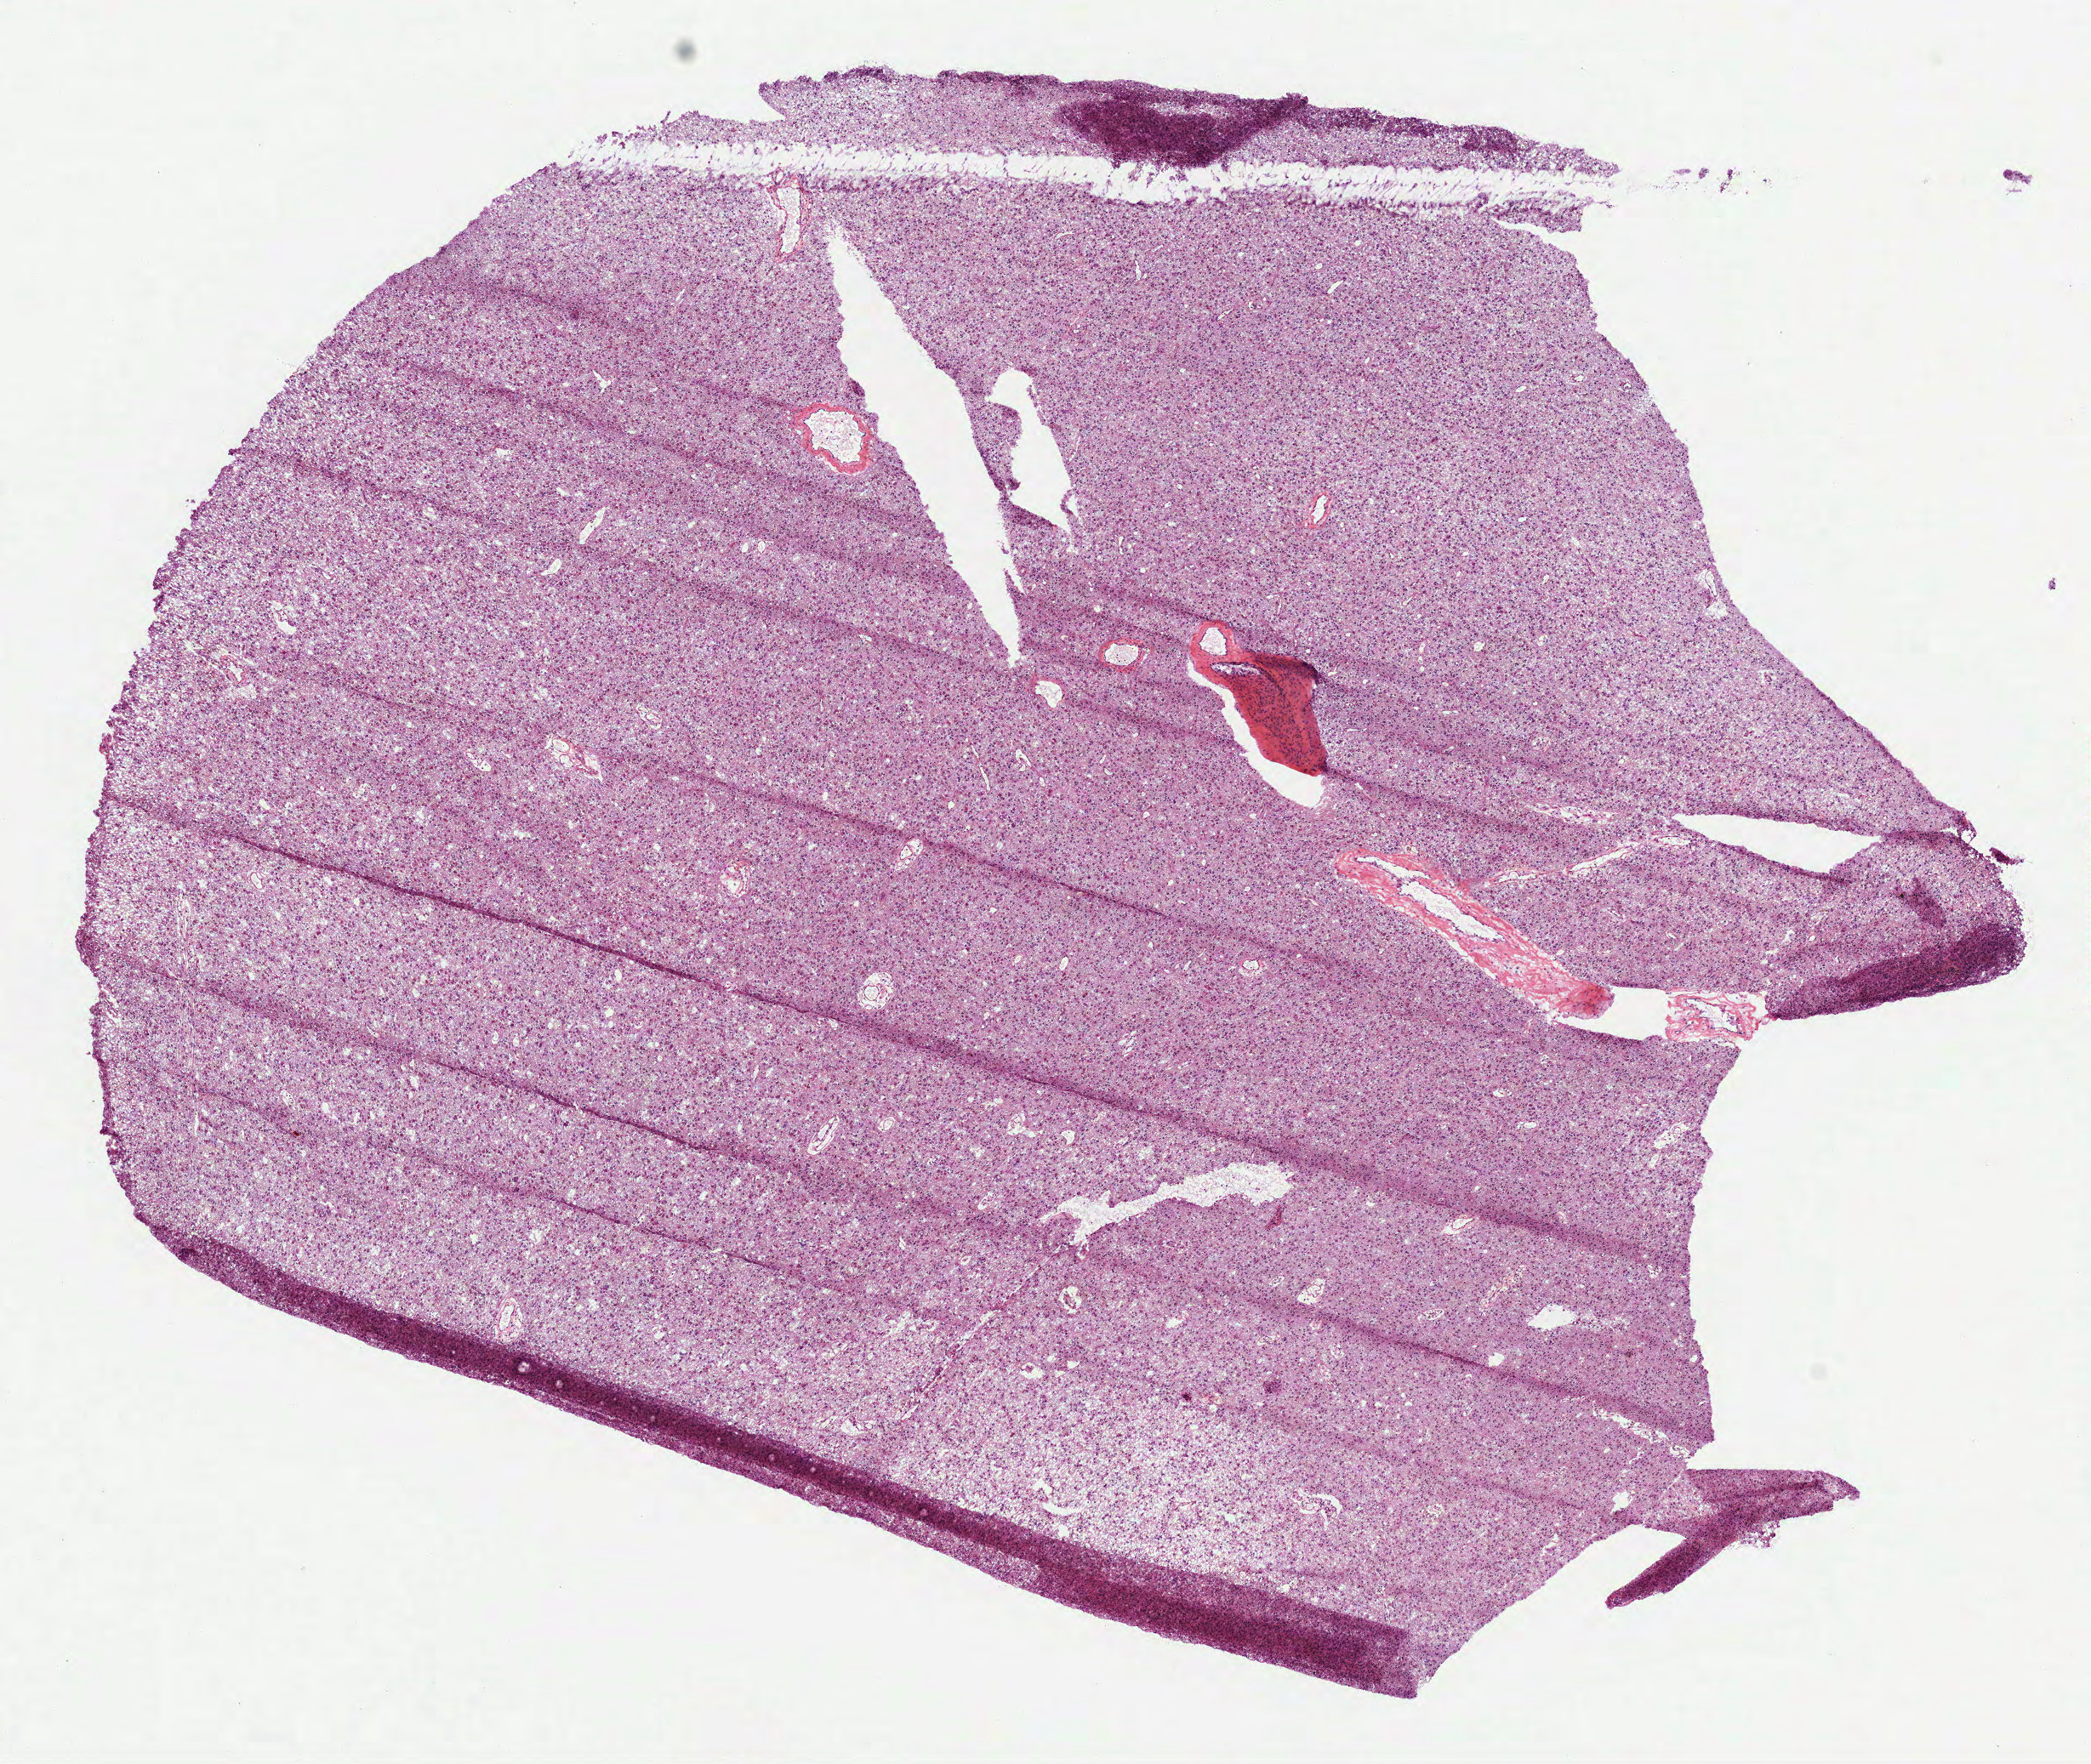
Digitized Hematoxylin and eosin (H&E) stained tissue section (whole slide), a low-resolution overview of the entire scanned area, about 9.9 x 8.4 mm; frozen section from the top of the tissue portion; primary tumour sample from the brain. Male, age 67 years at initial diagnosis. Histologic grade: G2 (moderately differentiated). Slide review estimates, as recorded: tumour cells 100%, tumour nuclei 75%, normal cells 0%, stromal cells 0%, necrosis 0%.
* laterality: right
* pathologic diagnosis: Mixed glioma (cerebrum)